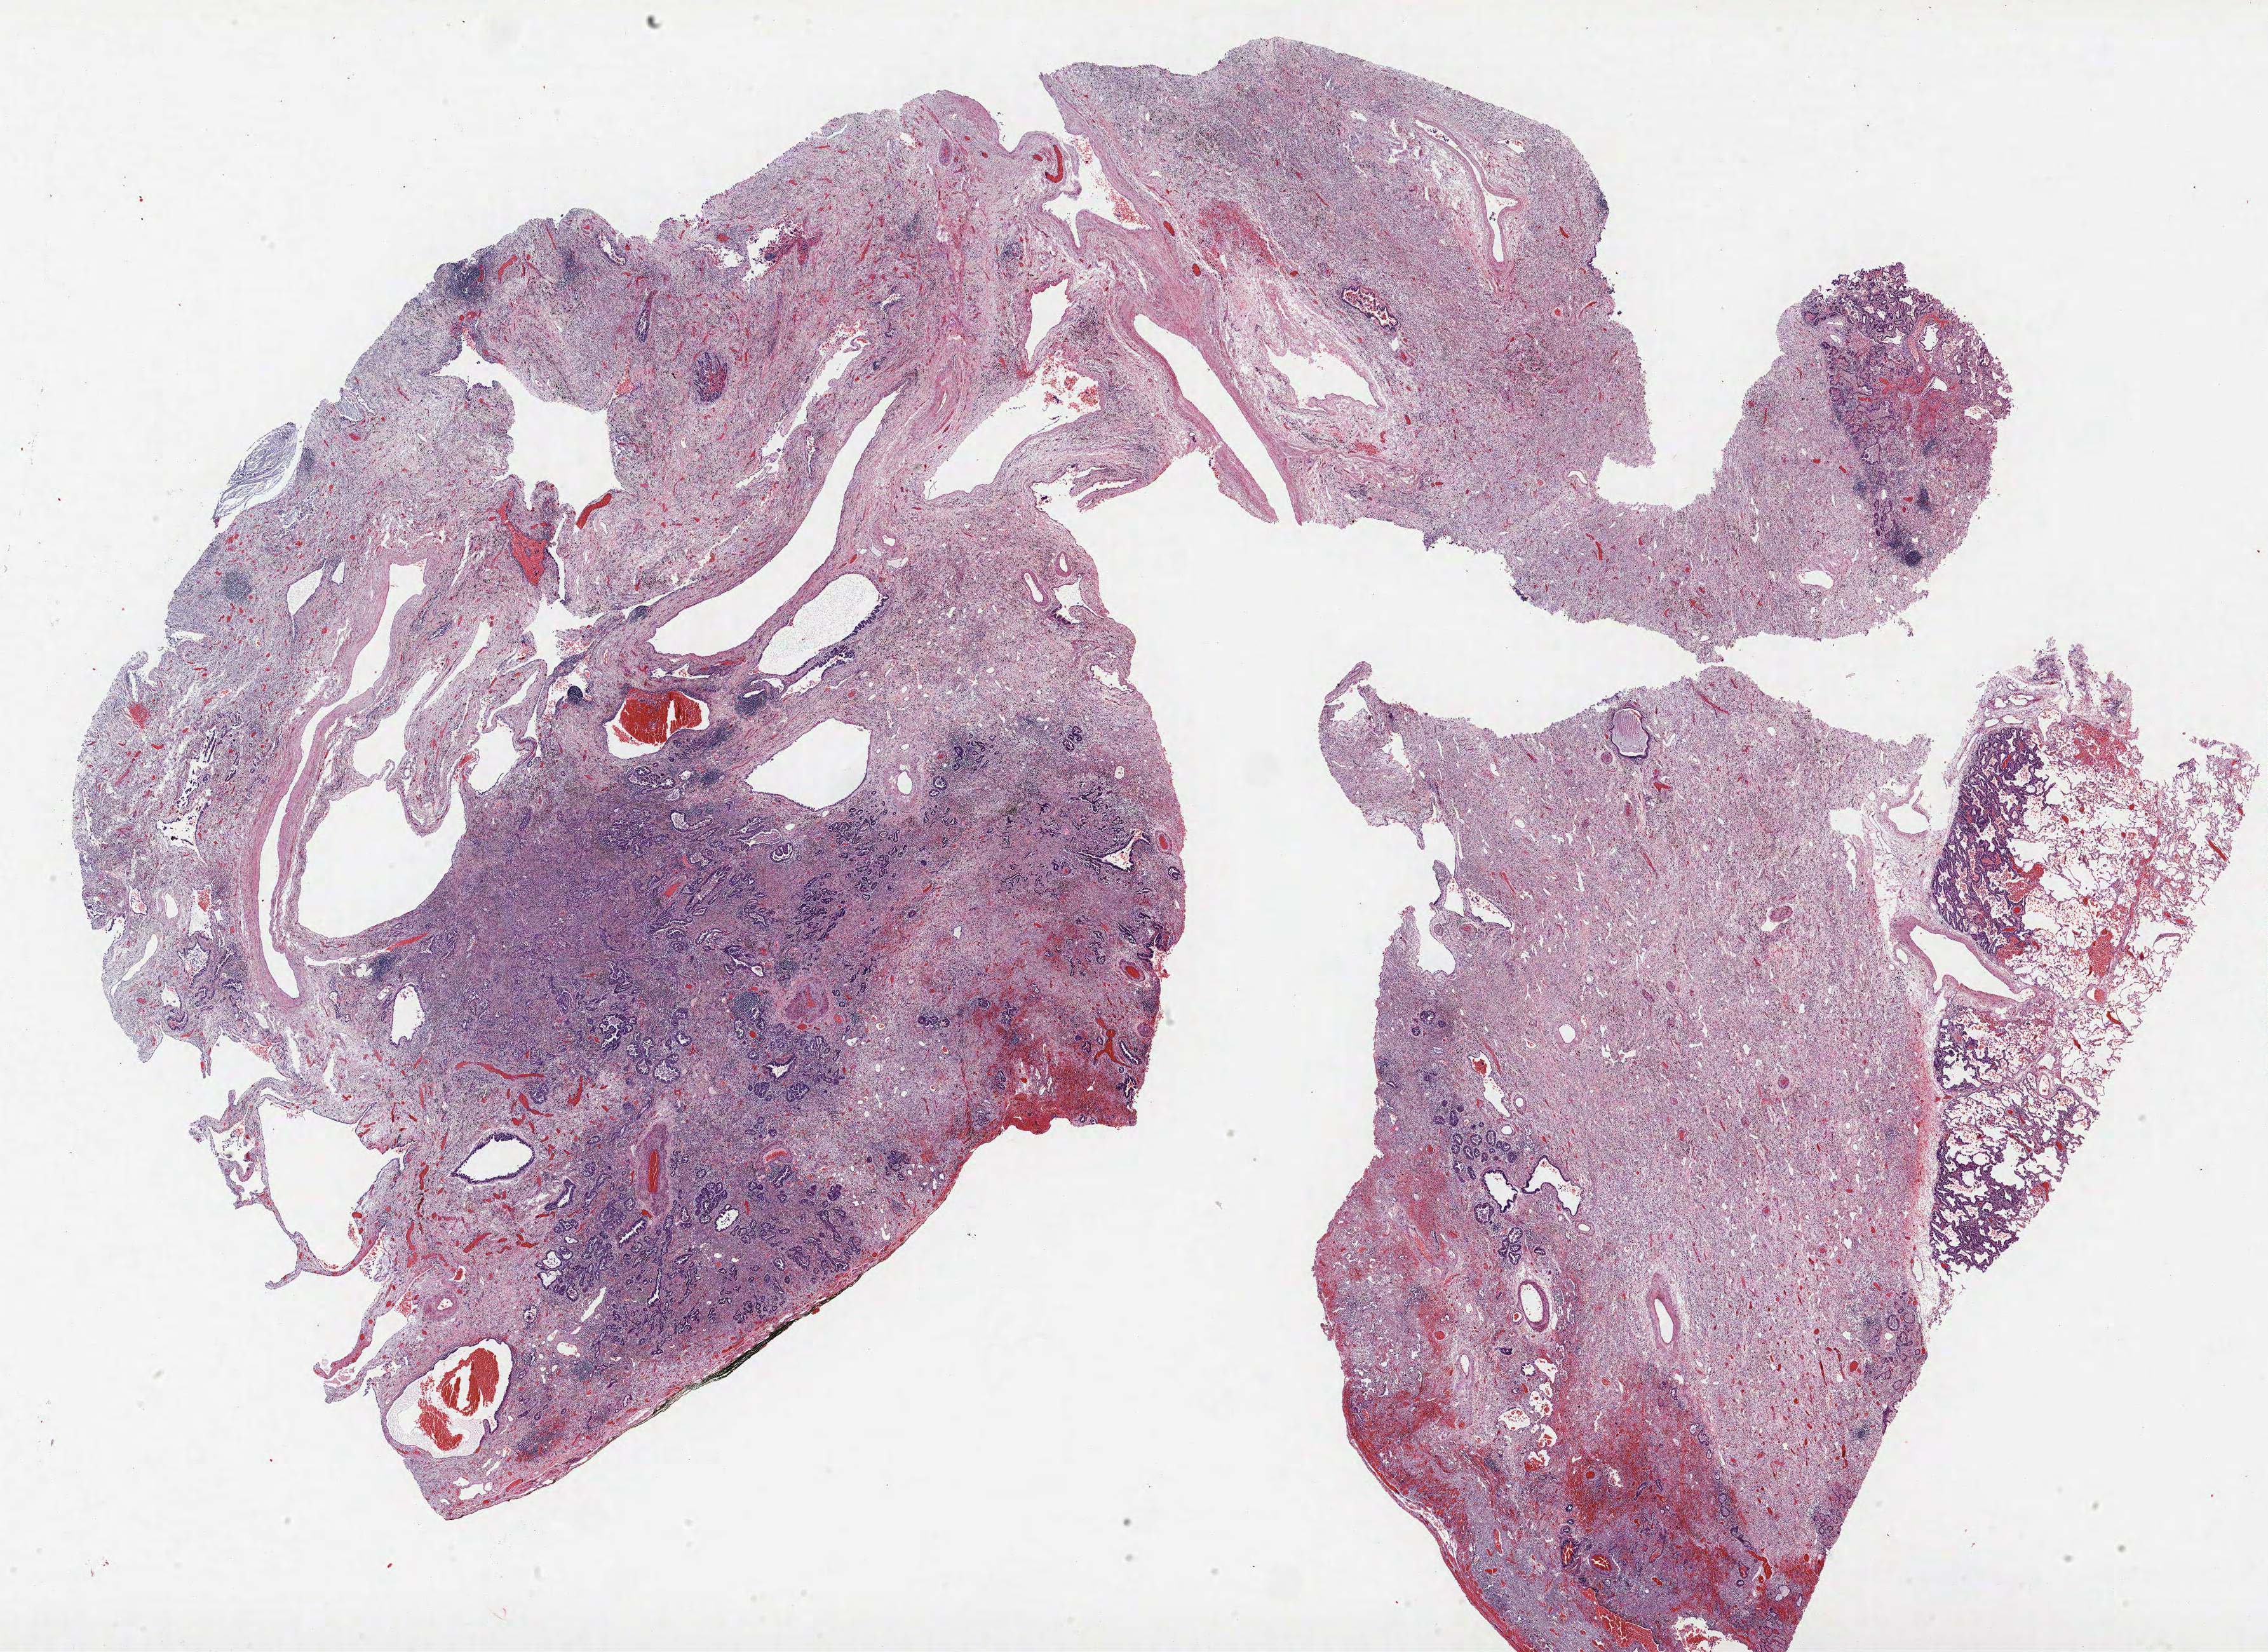
H&E whole-slide image — whole scanned area (about 28.6 x 20.8 mm) shown as a low-resolution overview; formalin-fixed paraffin-embedded (FFPE) section; lung tissue. Female, age 61 at enrolment. Current smoker at enrolment. Grade: well differentiated (G1).
Tumour size (pathology): 30 mm. Primary tumour location (clinical record): right upper lobe. Stage (AJCC 6th edition): IIIB. Participant's lung-cancer diagnosis: Adenocarcinoma, NOS. Note: participant had 2 primary lung cancers recorded; fields above describe the first.